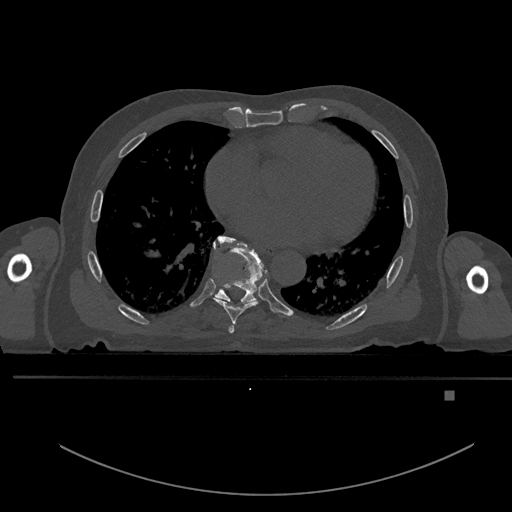
CT including the spine, one axial slice. Slice 231 of 969 in the series (ordered by position). Bone window (W 1800 / L 400 HU). 0.5 mm slice thickness. 512 × 512 image matrix, field of view 456 × 456 mm. Patient: male, 82 years. Case-level facts recorded for this patient, not image findings: primary cancer: prostate.
Outlined on this slice (semi-automatic segmentation, software-assisted and operator-edited):
- T6 vertebra: bounding box (x1, y1, x2, y2) in pixels: (228, 325, 234, 333)
- T7 vertebra: (214, 235, 268, 324)
- T8 vertebra: (213, 238, 263, 308)